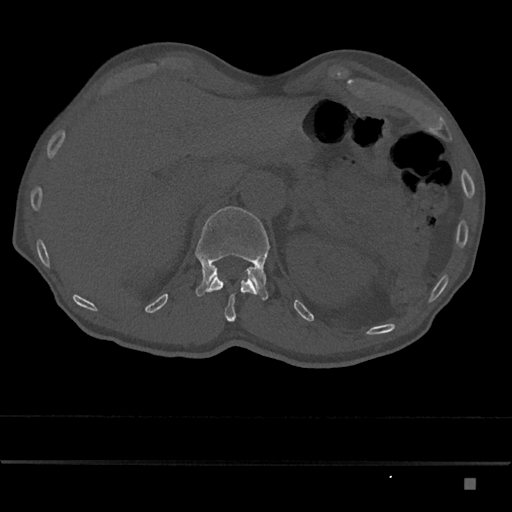
CT including the spine, one axial slice; slice 576 of 797 in the series (ordered by position); bone window (W 1800 / L 400 HU); 512 × 512 image matrix, field of view 390 × 390 mm. Male patient, age 72 years. Case-level facts recorded for this patient, not image findings: primary cancer: prostate.
Structures marked on this image (semi-automatic segmentation, software-assisted and operator-edited):
- L1 vertebra: bounding box [x1, y1, x2, y2] px = [195, 206, 270, 301]
- T12 vertebra: [206, 275, 256, 322]